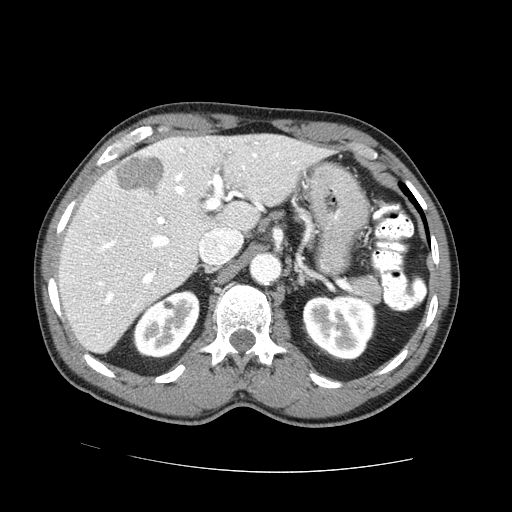
Contrast-enhanced abdominal CT (liver protocol), one axial slice; position 46 of 73 along the scan axis; reconstruction kernel STANDARD; one of 2 acquisitions stored at this slice position; soft-tissue window (W 400 / L 40 HU); 2.5 mm slice thickness; 512 × 512 image matrix. From the clinical record (not read from this slice): diagnosis: hepatocellular carcinoma (patient treated with transarterial chemoembolisation; whether this scan precedes or follows treatment is not stated here); TNM stage (as recorded): Stage-IVA; Child-Pugh class: A; tumour differentiation: no biopsy.
Annotated regions visible in this slice (semi-automatically segmented with operator editing):
- liver parenchyma outside the tumour (the mass and vessels are separate outlines, so this box may not span the whole liver): bounding box [x1, y1, x2, y2] px = [58, 134, 324, 352]
- mass: [114, 156, 163, 191]
- liver vessels: [95, 142, 278, 336]